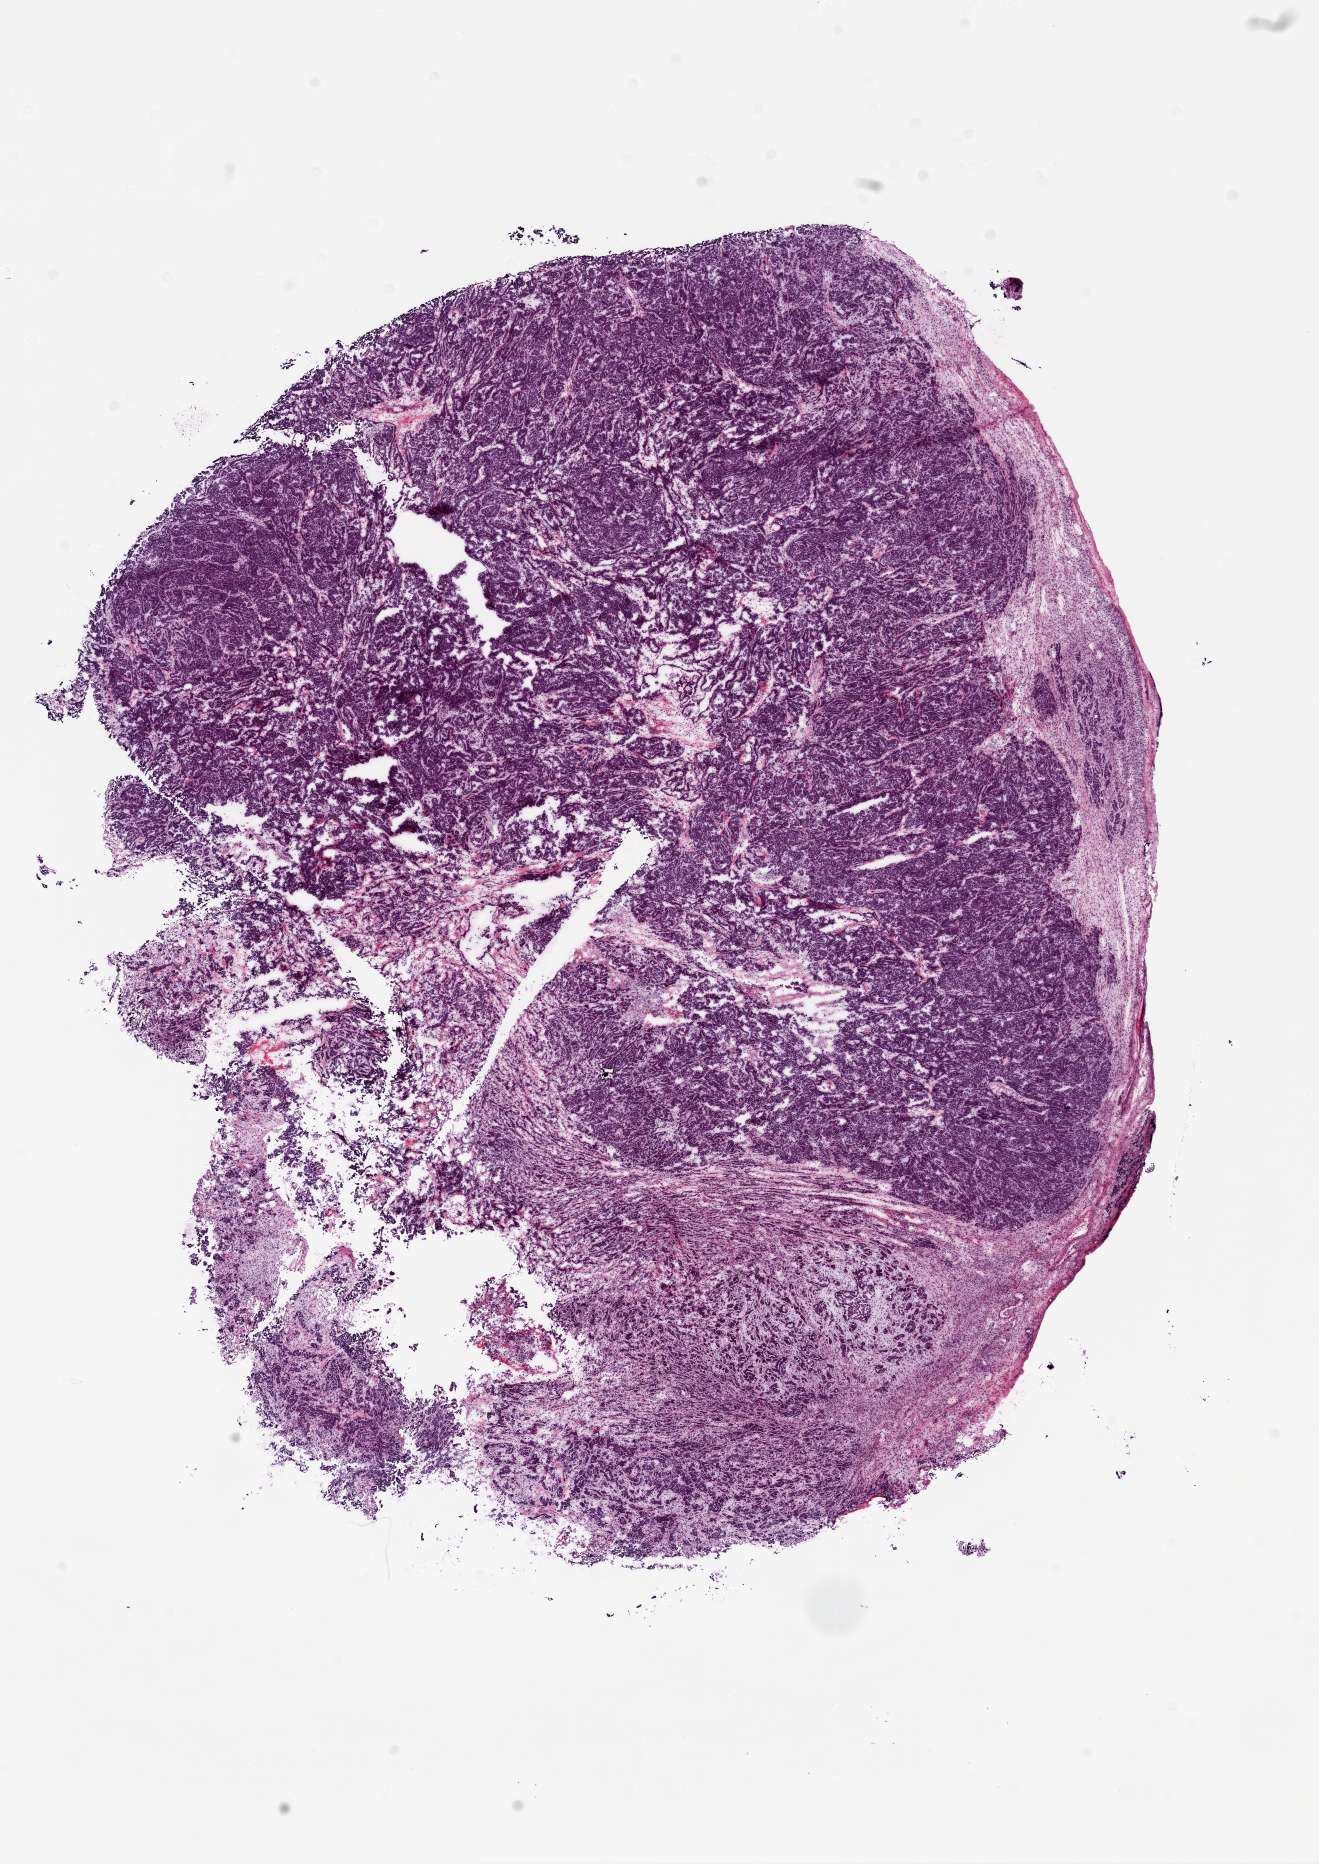
Whole-slide histology image, H&E-stained, a low-resolution overview of the entire scanned area, about 10.6 x 15.0 mm, frozen section from the top of the tissue portion, primary tumour sample from the ovary. Patient: female, age at initial diagnosis 71 years. Histologic grade: G3 (poorly differentiated). Composition of this section per pathologist review: tumour cells 80%, tumour nuclei 95%, normal cells 10%, stromal cells 10%, necrosis 0%.
- FIGO stage: IIIC
- diagnosis: Serous cystadenocarcinoma, NOS